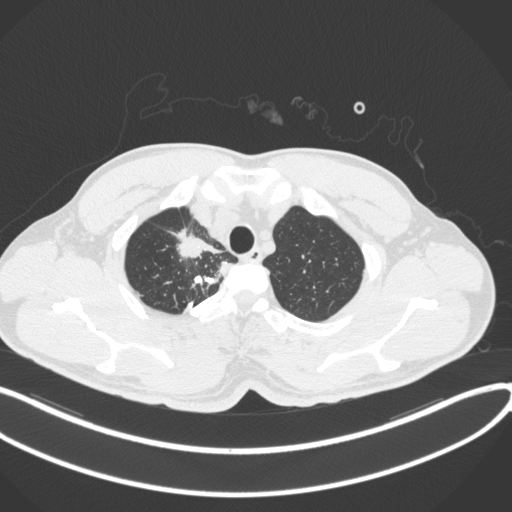
Chest CT, one axial slice; position 328 of 391 along the scan axis; 120 kVp; lung window (W 1500 / L -600 HU); 1 mm slice thickness; 512 × 512 image matrix. Male patient, age 48 years. From the clinical record (not read from this slice): clinical TNM (as recorded): T1c N1 M1.
Structures marked on this image (bounding box drawn by a radiologist):
- lung tumour (recorded histology: adenocarcinoma): bounding box (x1, y1, x2, y2) in pixels: (173, 228, 223, 261)